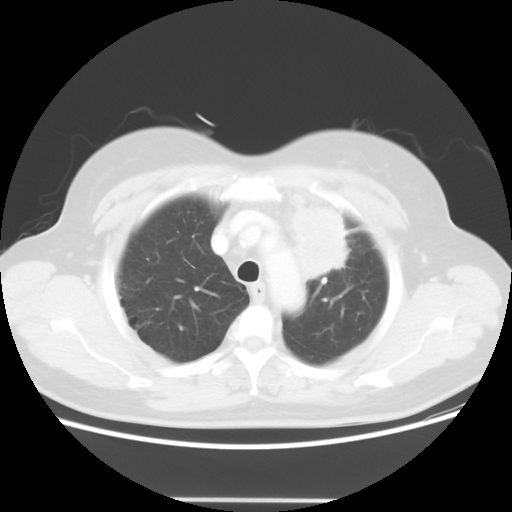
Chest CT, one axial slice; slice 43 of 52 in the series (ordered by position); reconstruction kernel STANDARD; 120 kVp; lung window (W 1500 / L -600 HU); 5 mm slice thickness; 512 × 512 image matrix. Patient: female, 52 years. From the clinical record (not read from this slice): clinical TNM (as recorded): T2 N3 M0.
Outlined on this slice (bounding box drawn by a radiologist):
- lung tumour (recorded histology: adenocarcinoma): box from (x=284, y=192) to (x=351, y=278) px